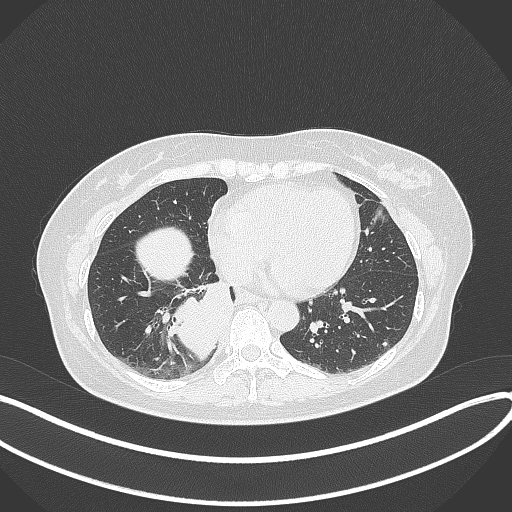
Chest CT, one axial slice. Position 123 of 331 along the scan axis. Reconstruction kernel B70f. Lung window (W 1500 / L -600 HU). 512 × 512 image matrix. Female patient, age 54 years. From the clinical record (not read from this slice): clinical TNM (as recorded): T4 N0 M0.
Annotated regions visible in this slice (bounding box drawn by a radiologist):
- lung tumour (recorded histology: adenocarcinoma): bounding box [x1, y1, x2, y2] px = [168, 271, 239, 364]